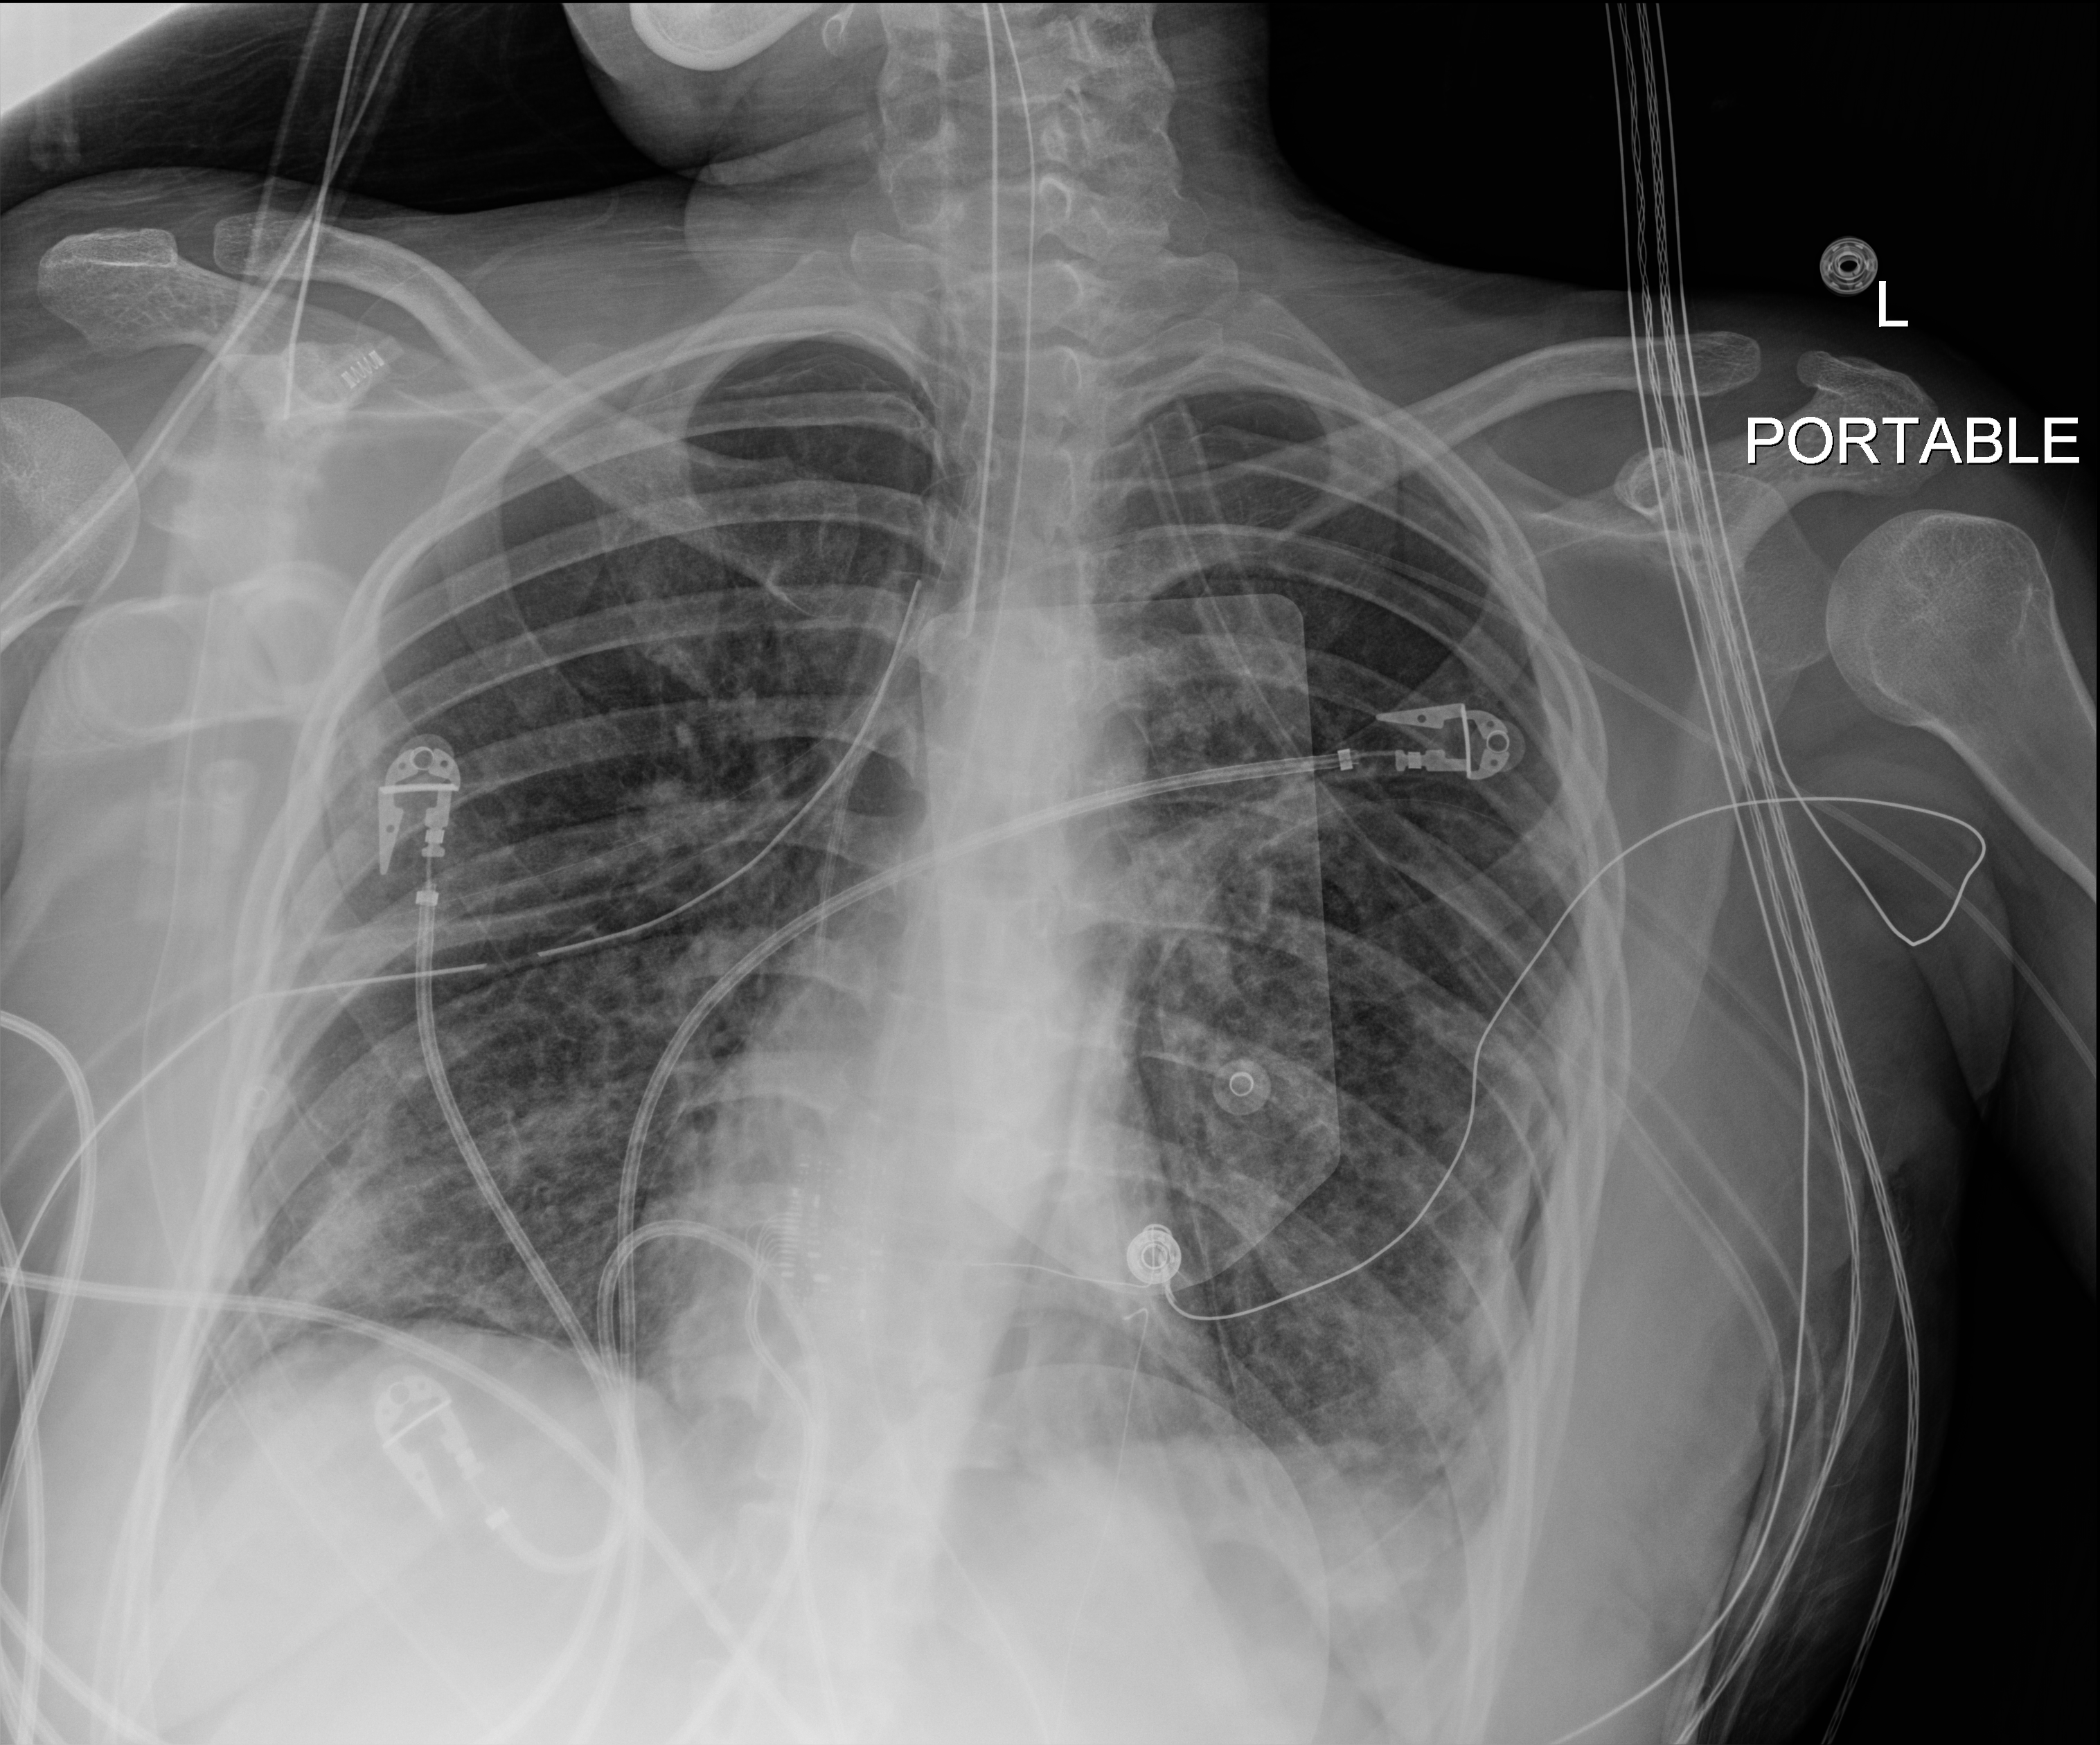
Chest X-ray (portable), anteroposterior (AP) projection. Patient hospitalised with COVID-19, aged 18–59 years.
Admission-level facts for this patient (not findings on this image; timing relative to this image not recorded):
- mechanically ventilated during this hospital stay: yes
- length of hospital stay: 30 days